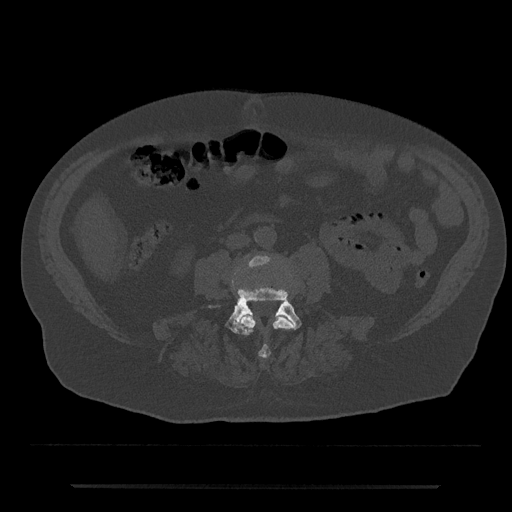
CT including the spine, one axial slice. Slice 373 of 797 in the series (ordered by position). Reconstruction kernel Br40s/3. 120 kVp. Bone window (W 1800 / L 400 HU). 512 × 512 image matrix, field of view 434 × 434 mm. Patient: male, 80 years. Case-level facts recorded for this patient, not image findings: primary cancer: prostate.
Structures marked on this image (semi-automatic segmentation, software-assisted and operator-edited):
- L3 vertebra: bounding box <237,255,294,358> (left, top, right, bottom; pixels)
- L4 vertebra: <209,286,302,333>